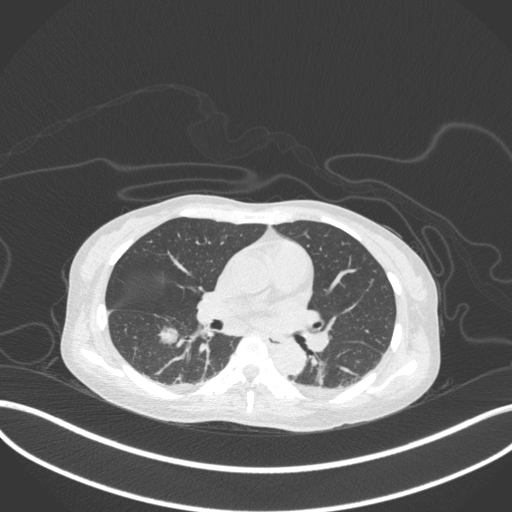
Chest CT, one axial slice; position 164 of 260 along the scan axis; lung window (W 1500 / L -600 HU); 1 mm slice thickness; 512 × 512 image matrix. Female patient, age 44 years. From the clinical record (not read from this slice): clinical TNM (as recorded): T1c N0 M0.
Annotated regions visible in this slice (rectangle marked by the reading radiologist):
- lung tumour (recorded histology: adenocarcinoma): bounding box (x1, y1, x2, y2) in pixels: (158, 325, 180, 348)